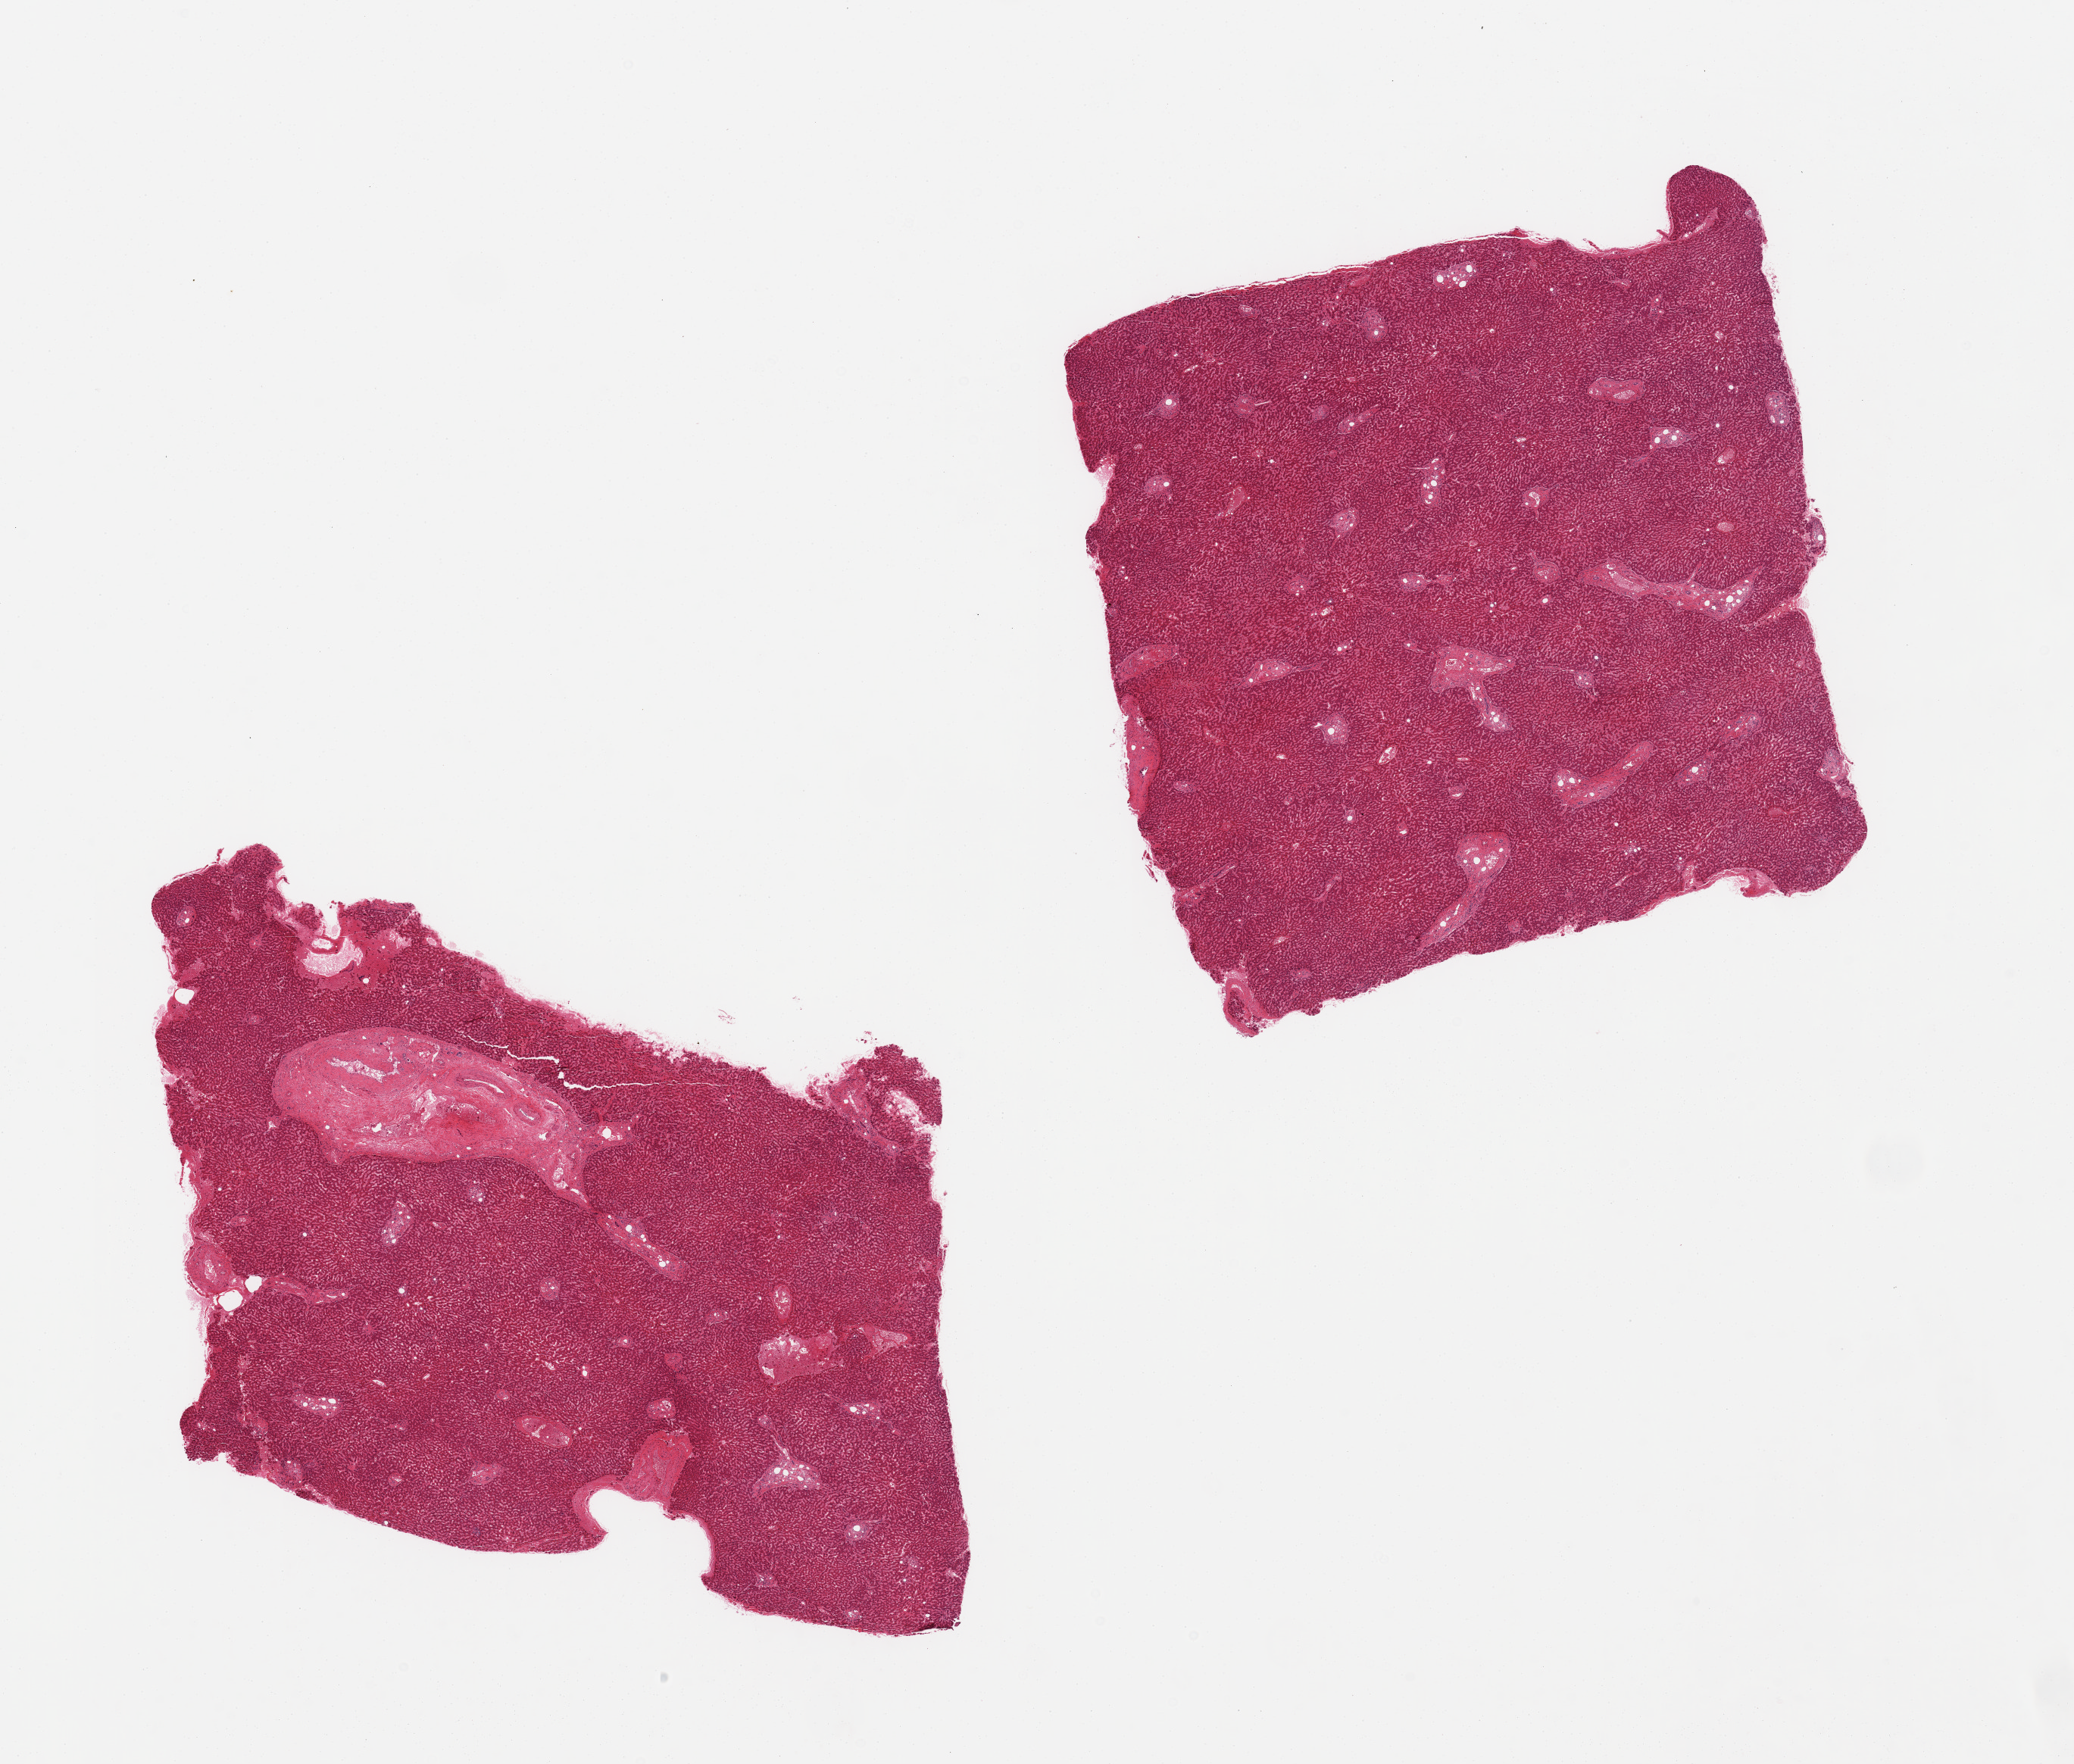
Whole-slide image, H&E stain — a low-resolution overview of the entire scanned area, about 21.7 x 18.4 mm; PAXgene-fixed paraffin-embedded (PFPE) section; target tissue: liver; tissue donor sample. Donor: male.
- reviewer comment on this tissue sample: 2 pieces, mild congestion, minimal fat